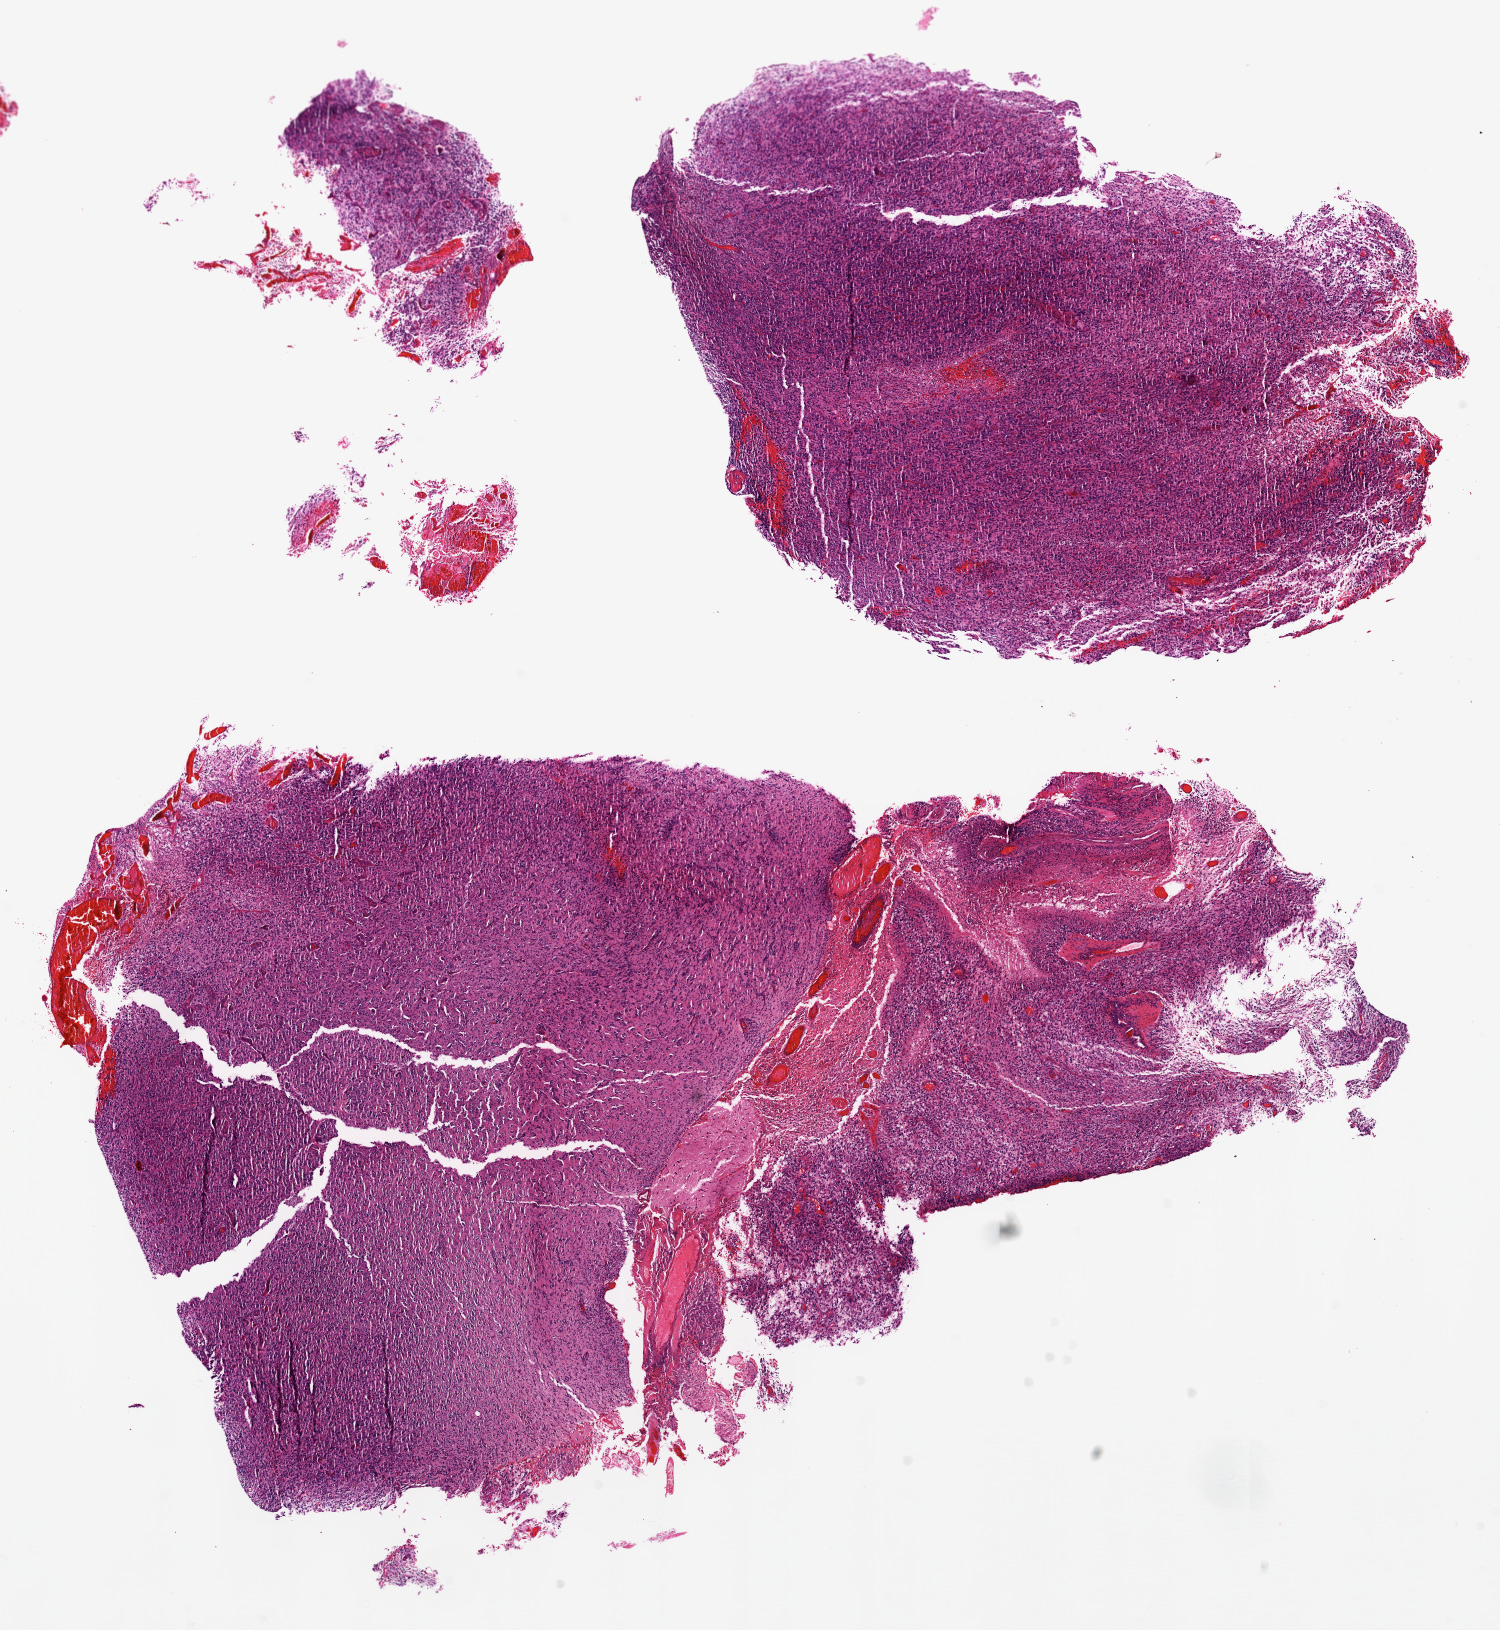
Digitized Hematoxylin and eosin (H&E) stained tissue section (whole slide) — whole scanned area (about 12.0 x 13.1 mm) shown as a low-resolution overview. FFPE section. Brain, primary tumour sample. Female, age 77 years at initial diagnosis.
Pathologic diagnosis: Glioblastoma.